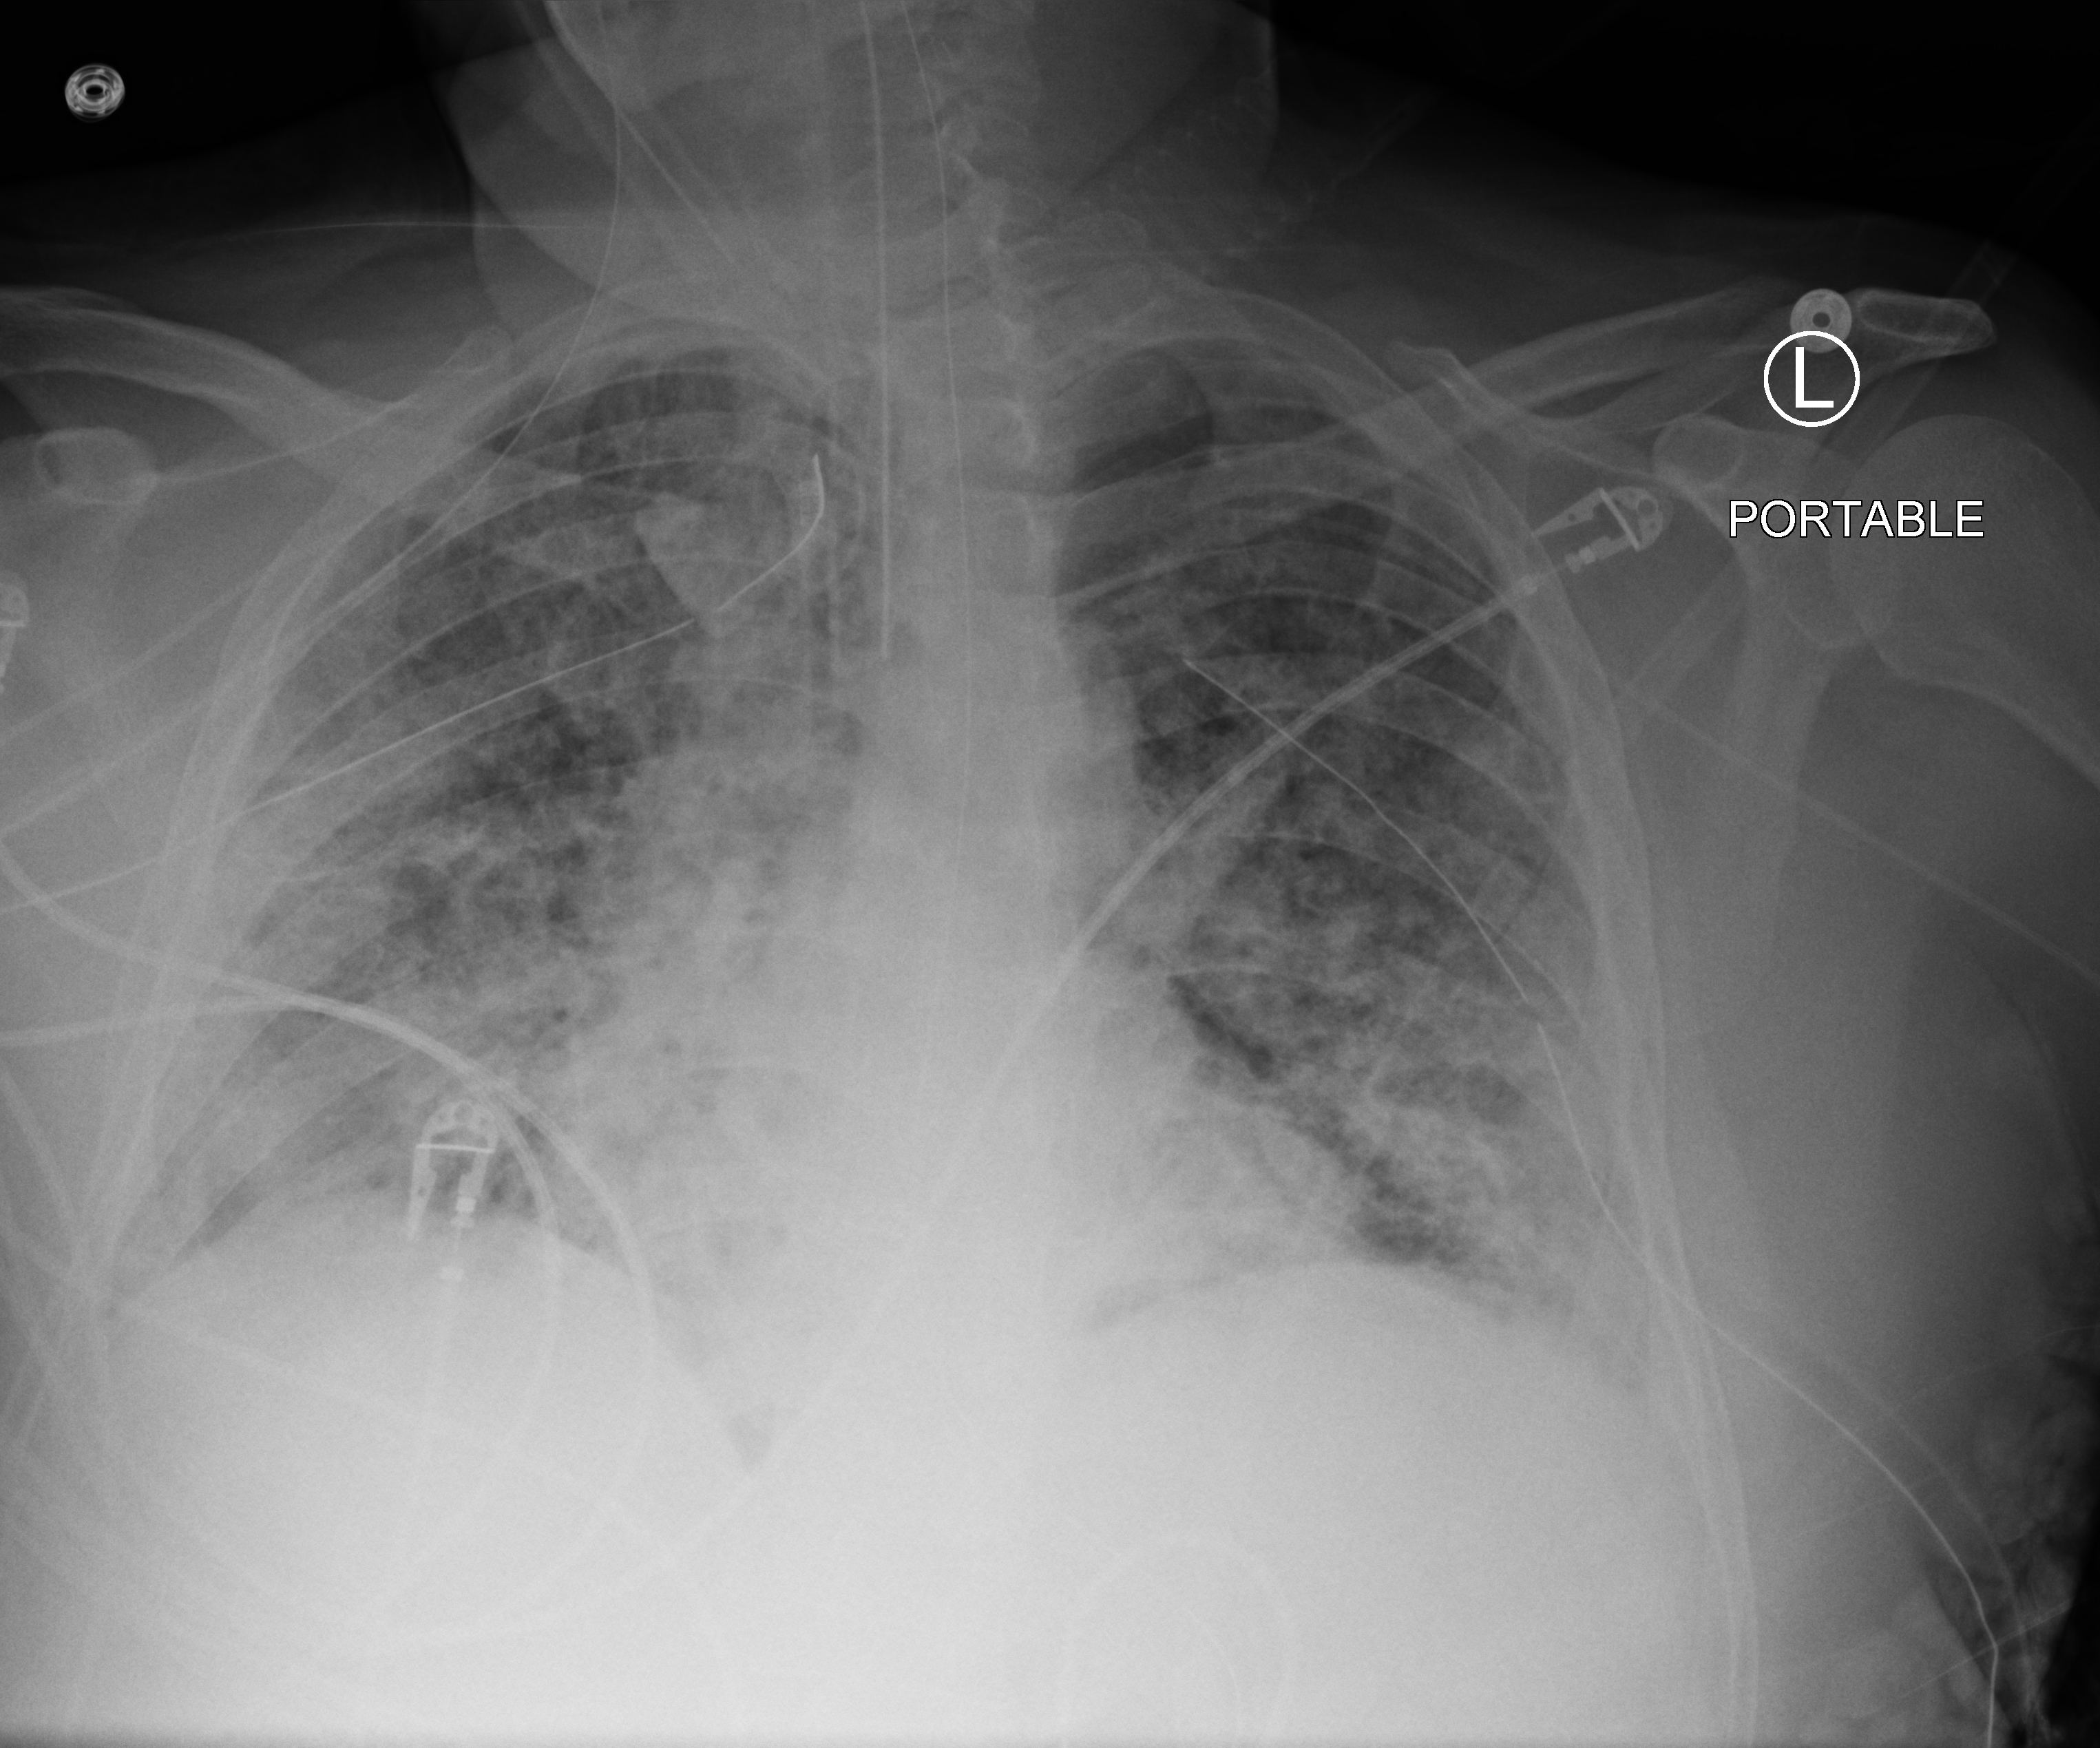
Chest X-ray (portable); anteroposterior (AP) projection. Male patient hospitalised with COVID-19, age 18–59 years.
From the hospital-stay record, not from the radiograph (when in the stay this image was taken is not recorded):
- admitted to intensive care during this hospital stay: yes
- mechanically ventilated during this hospital stay: yes